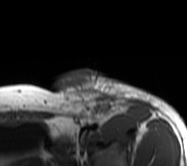
MRI of an extremity soft-tissue mass, one axial slice. MR volume resampled by the dataset authors to the PET/CT grid (not the native acquisition matrix). 3.27 mm slice thickness. 187 × 166 image matrix, field of view 183 × 162 mm. Female patient. Case-level facts recorded for this patient, not image findings: histological type: leiomyosarcoma; grade: high; site of the primary tumour: groin.
Annotated regions visible in this slice (expert contour drawn on MRI and transferred to this co-registered scan by the dataset authors):
- gross tumour volume including surrounding oedema: box from (x=52, y=69) to (x=156, y=118) px
- gross tumour volume (mass): (x=57, y=71)–(x=110, y=118)